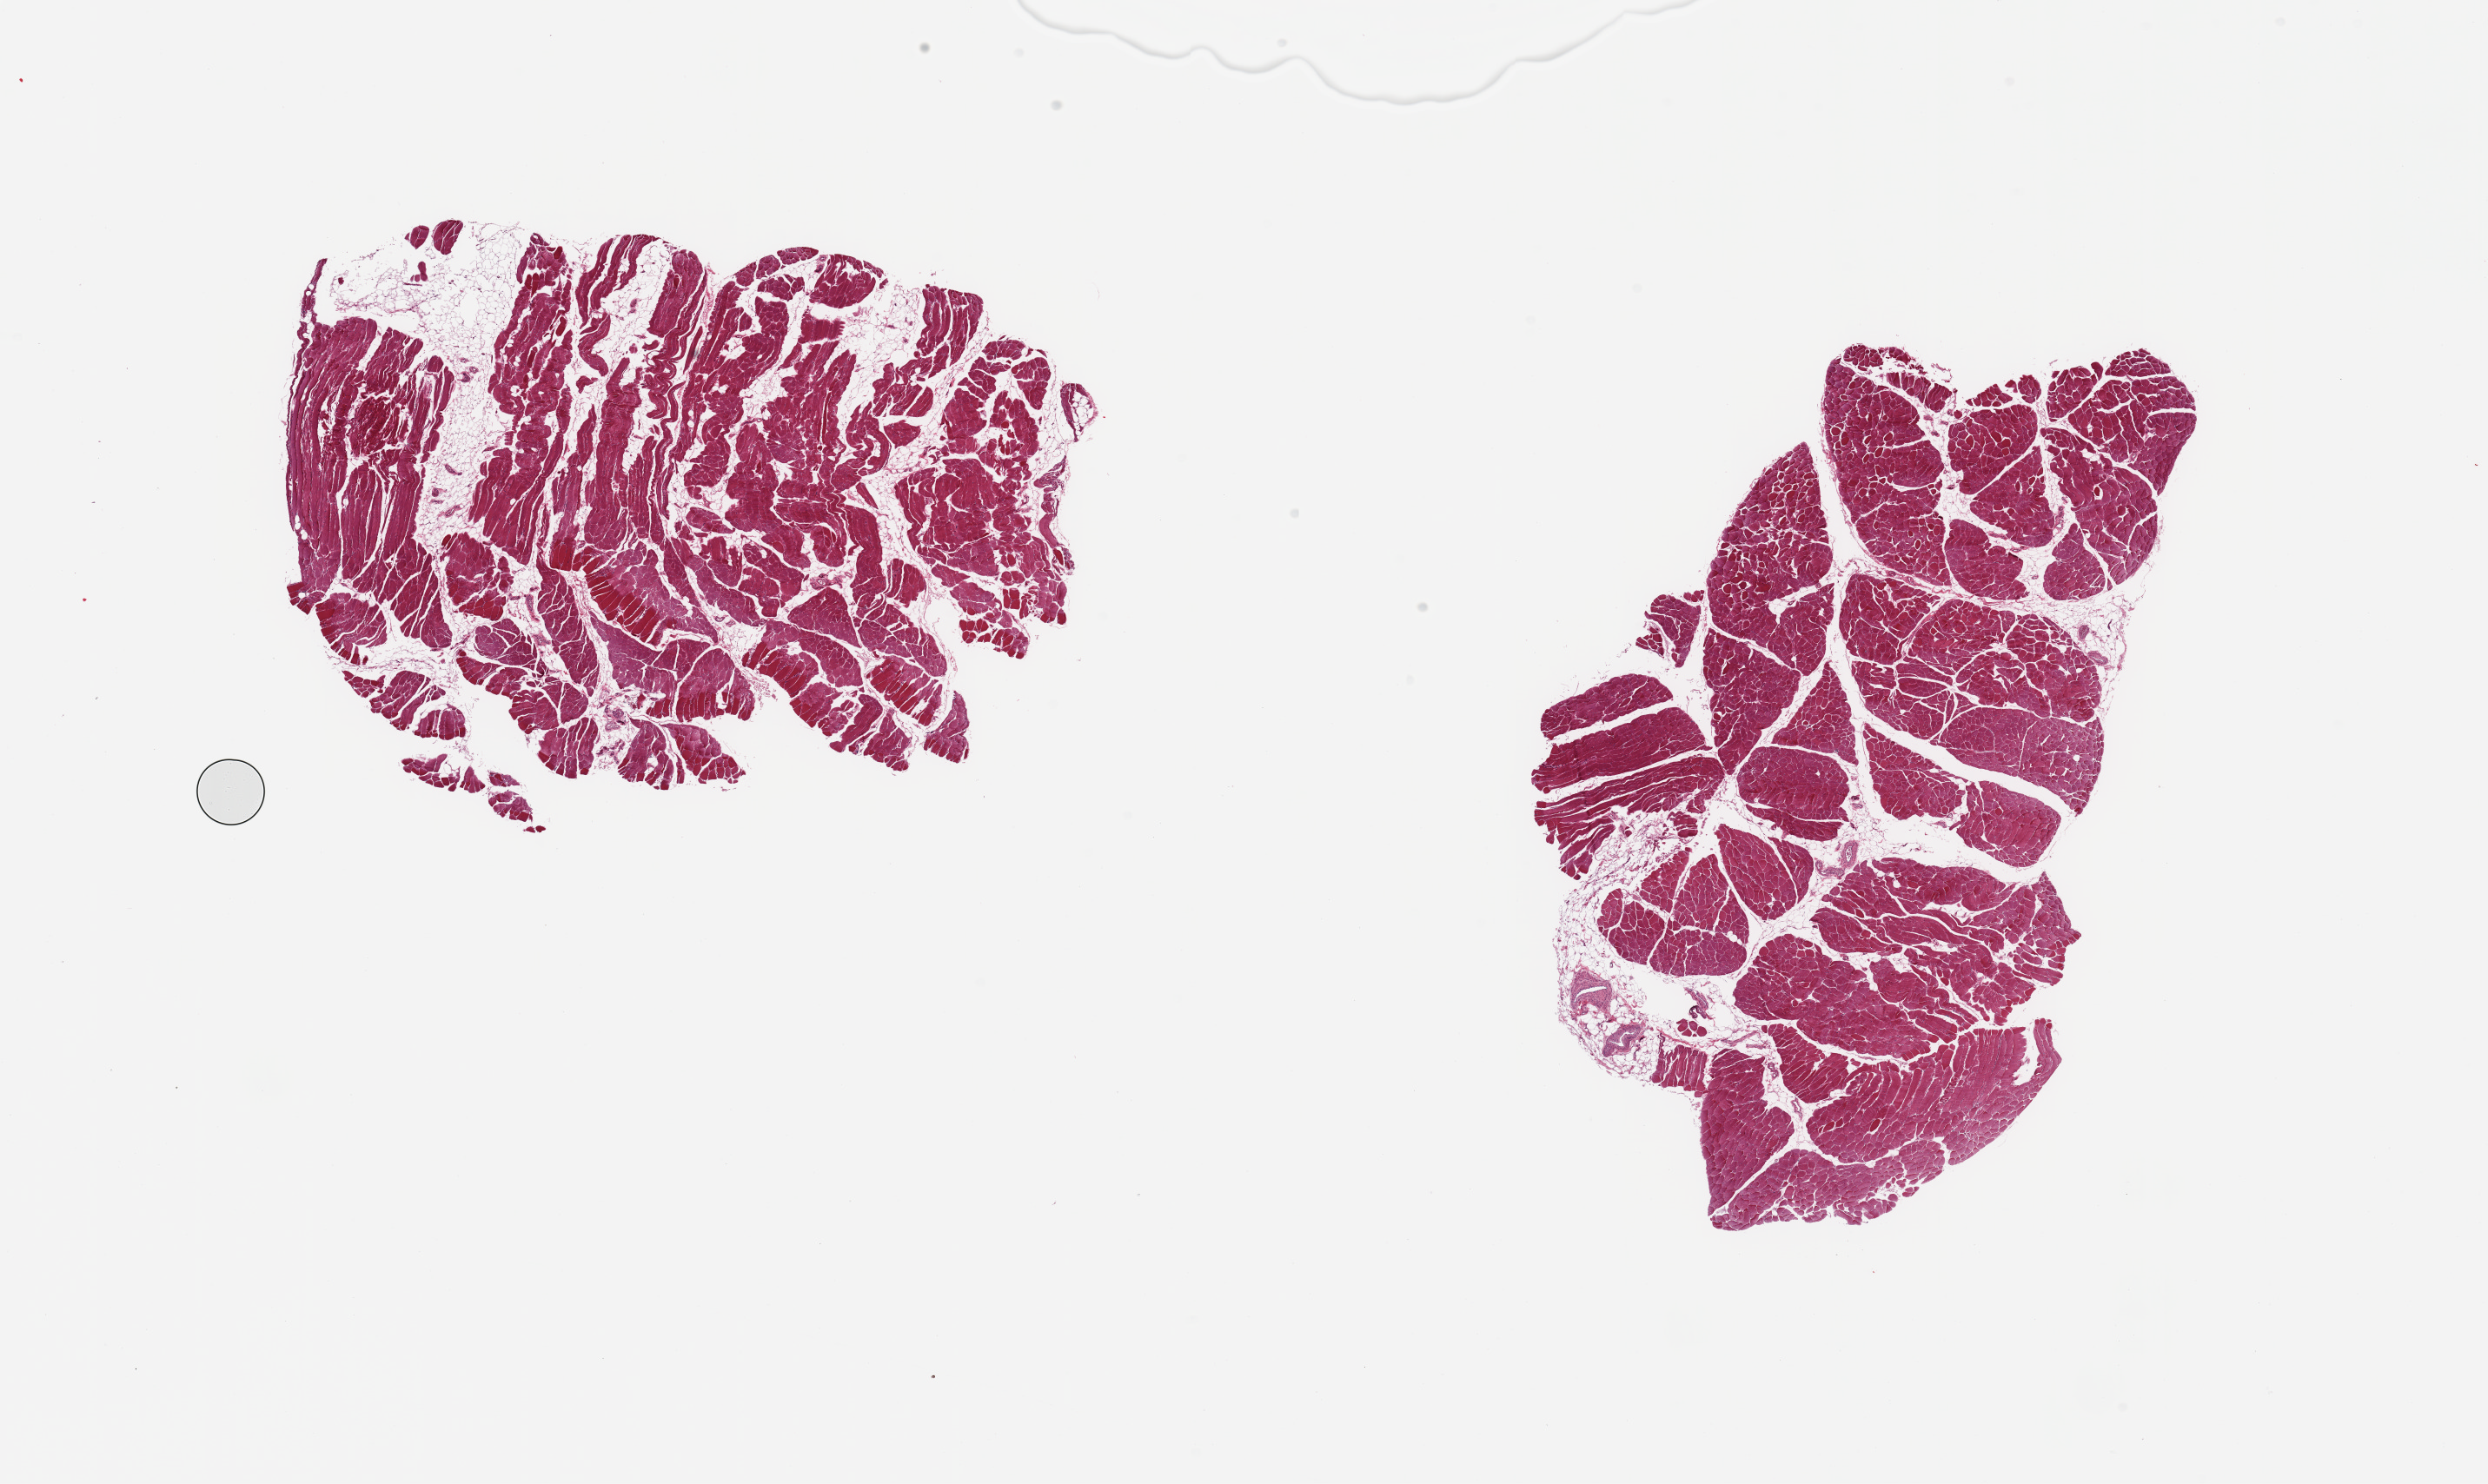
H&E whole-slide image, brightfield — whole scanned area (about 22.6 x 13.5 mm, from a 20x scan) shown as a low-resolution overview; PAXgene-fixed paraffin-embedded (PFPE) section; section of skeletal muscle (target tissue); donor tissue sample.
Pathologist's review note for this sample: 2 pieces; Muscle fibers mildly atrophic; interstitial fat is ~25-30% total tissue.